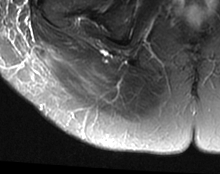
MRI of an extremity soft-tissue mass, one axial slice; T2-weighted fat-saturated; MR volume resampled by the dataset authors to the PET/CT grid (not the native acquisition matrix); 3.27 mm slice thickness; 220 × 174 image matrix. Female patient. From the clinical record (not read from this slice): histological type: spindle cell suggestive of myxofibrosarcoma; grade: intermediate; site of the primary tumour: right buttock.
Annotated regions visible in this slice (expert contour drawn on MRI and transferred to this co-registered scan by the dataset authors):
- gross tumour volume (mass): box from (x=45, y=45) to (x=99, y=92) px